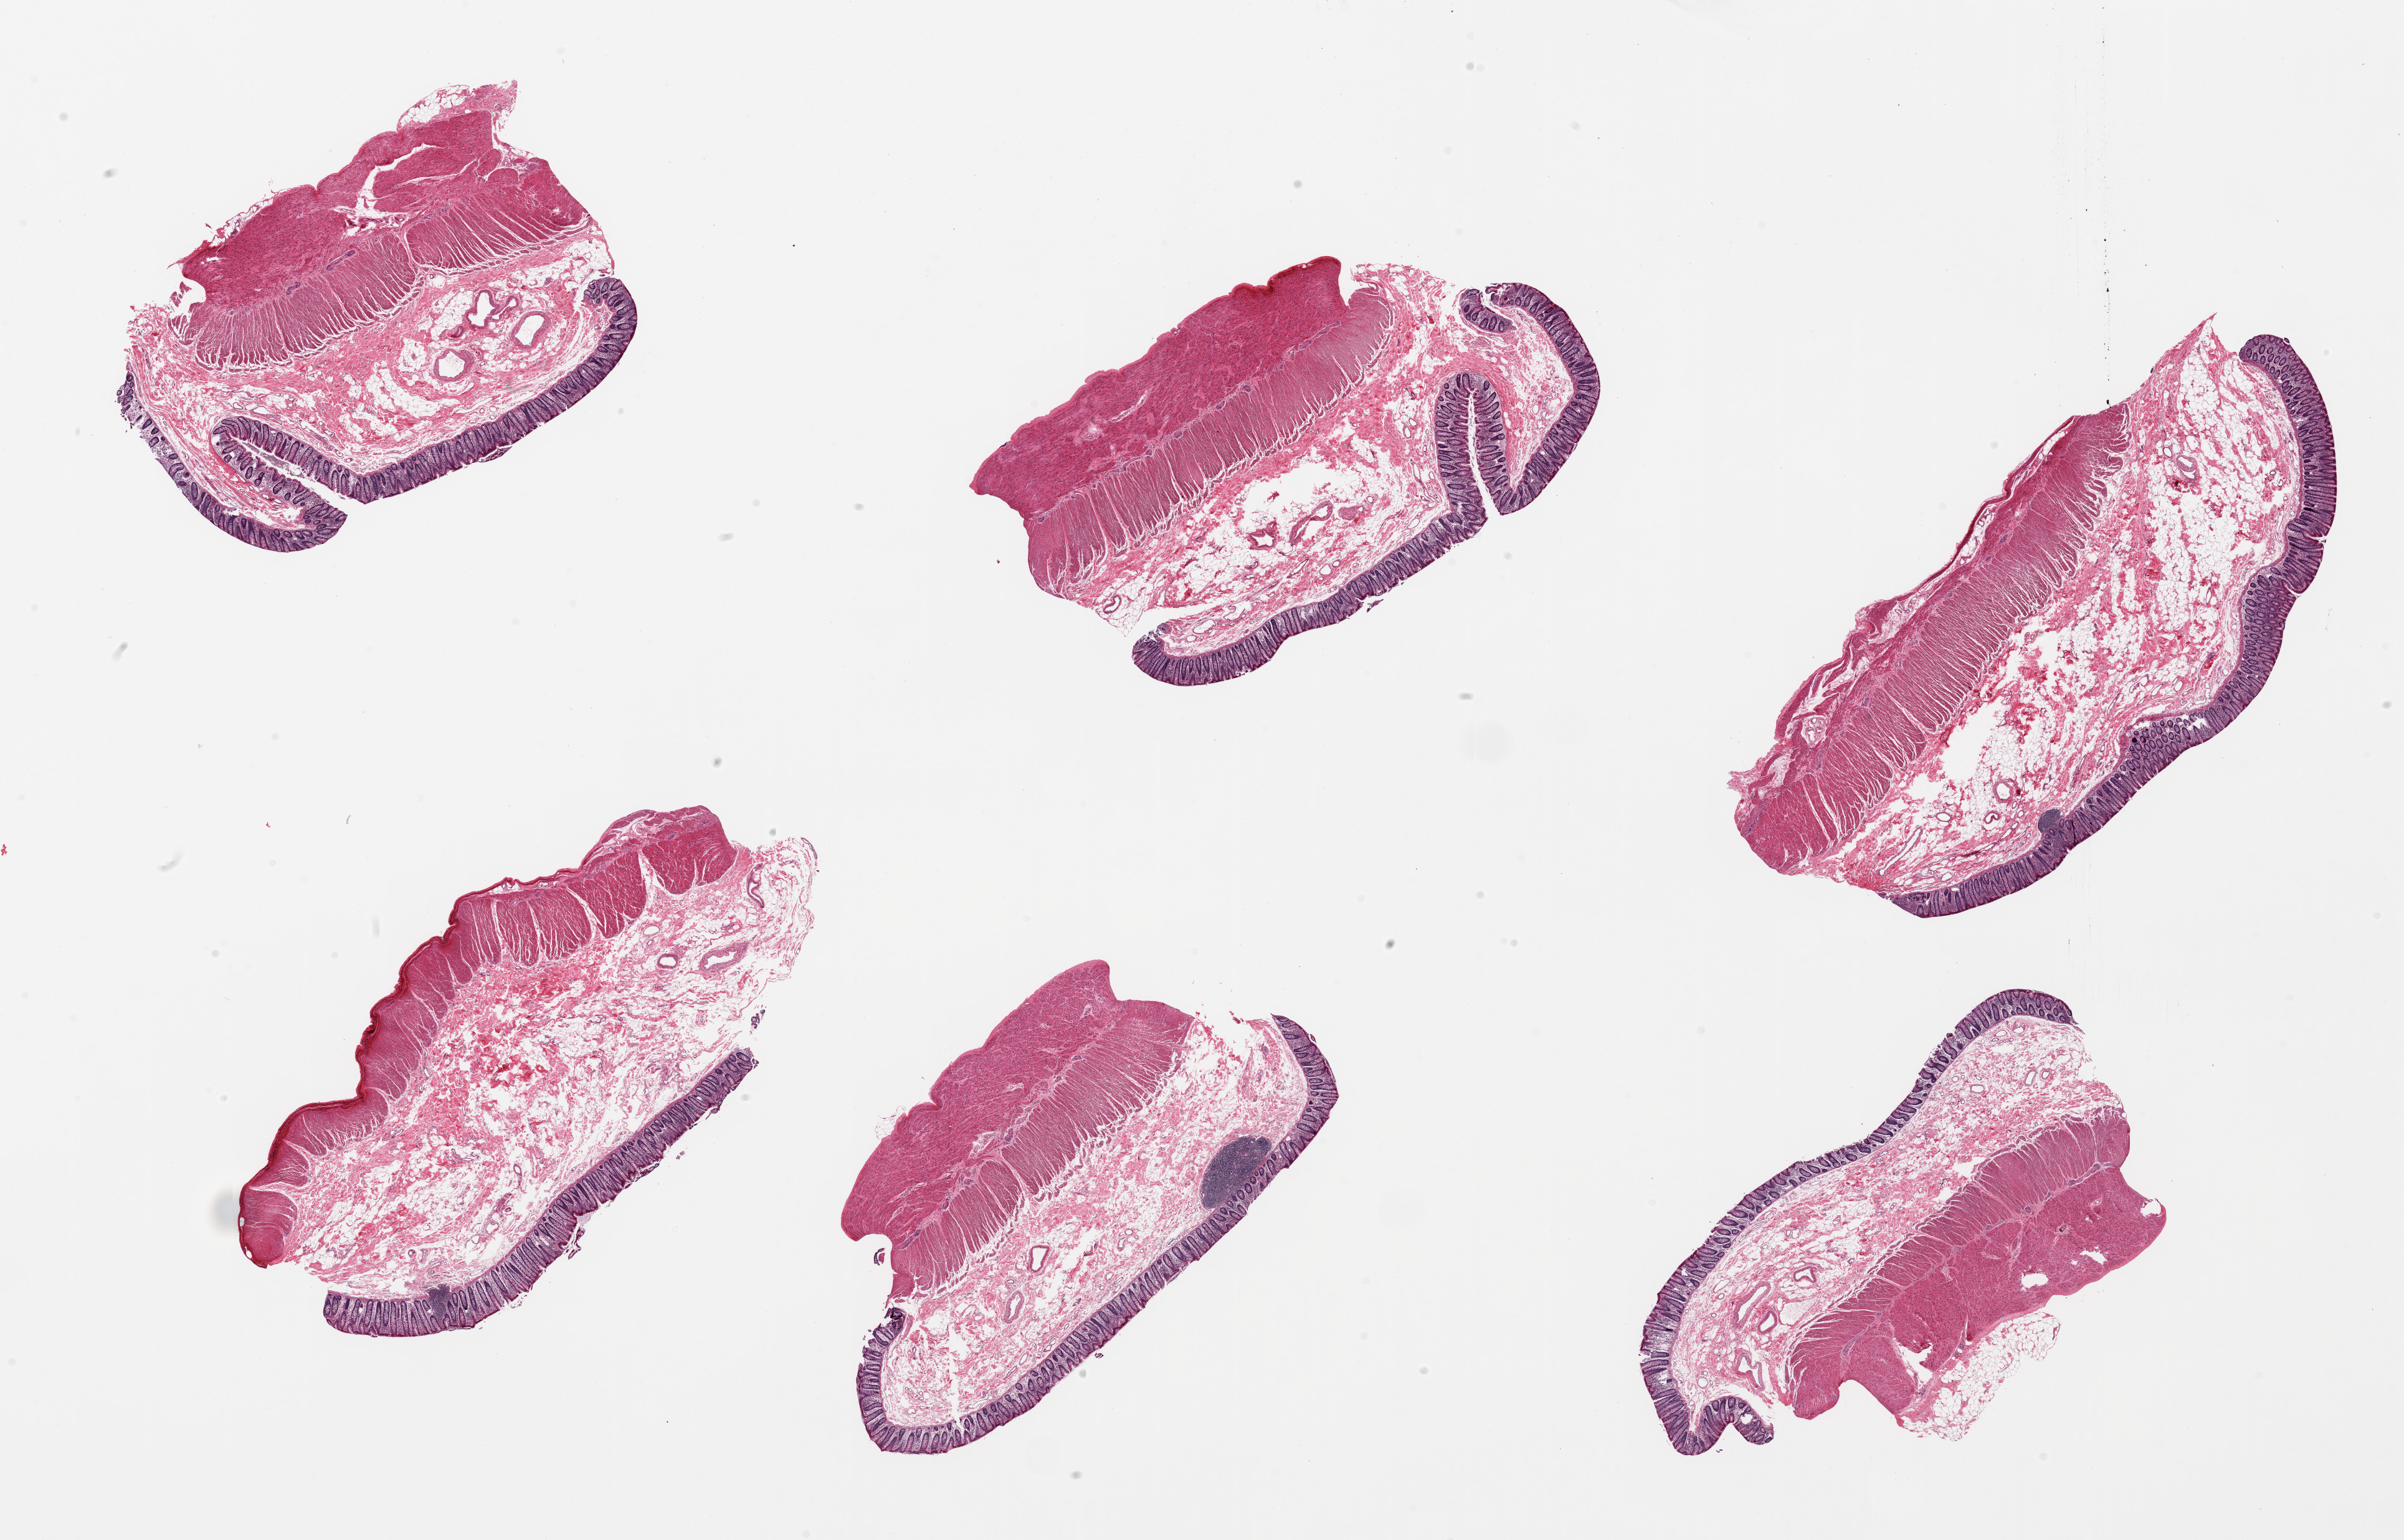
Whole-slide image, H&E stain, shown as a low-resolution overview of the whole scanned area (about 30.5 x 19.5 mm), PAXgene-fixed, paraffin-embedded tissue, target tissue: transverse colon, donor tissue sample. Donor: male.
Pathologist's review note for this sample: 6 pieces; full thickness sections, well preserved.